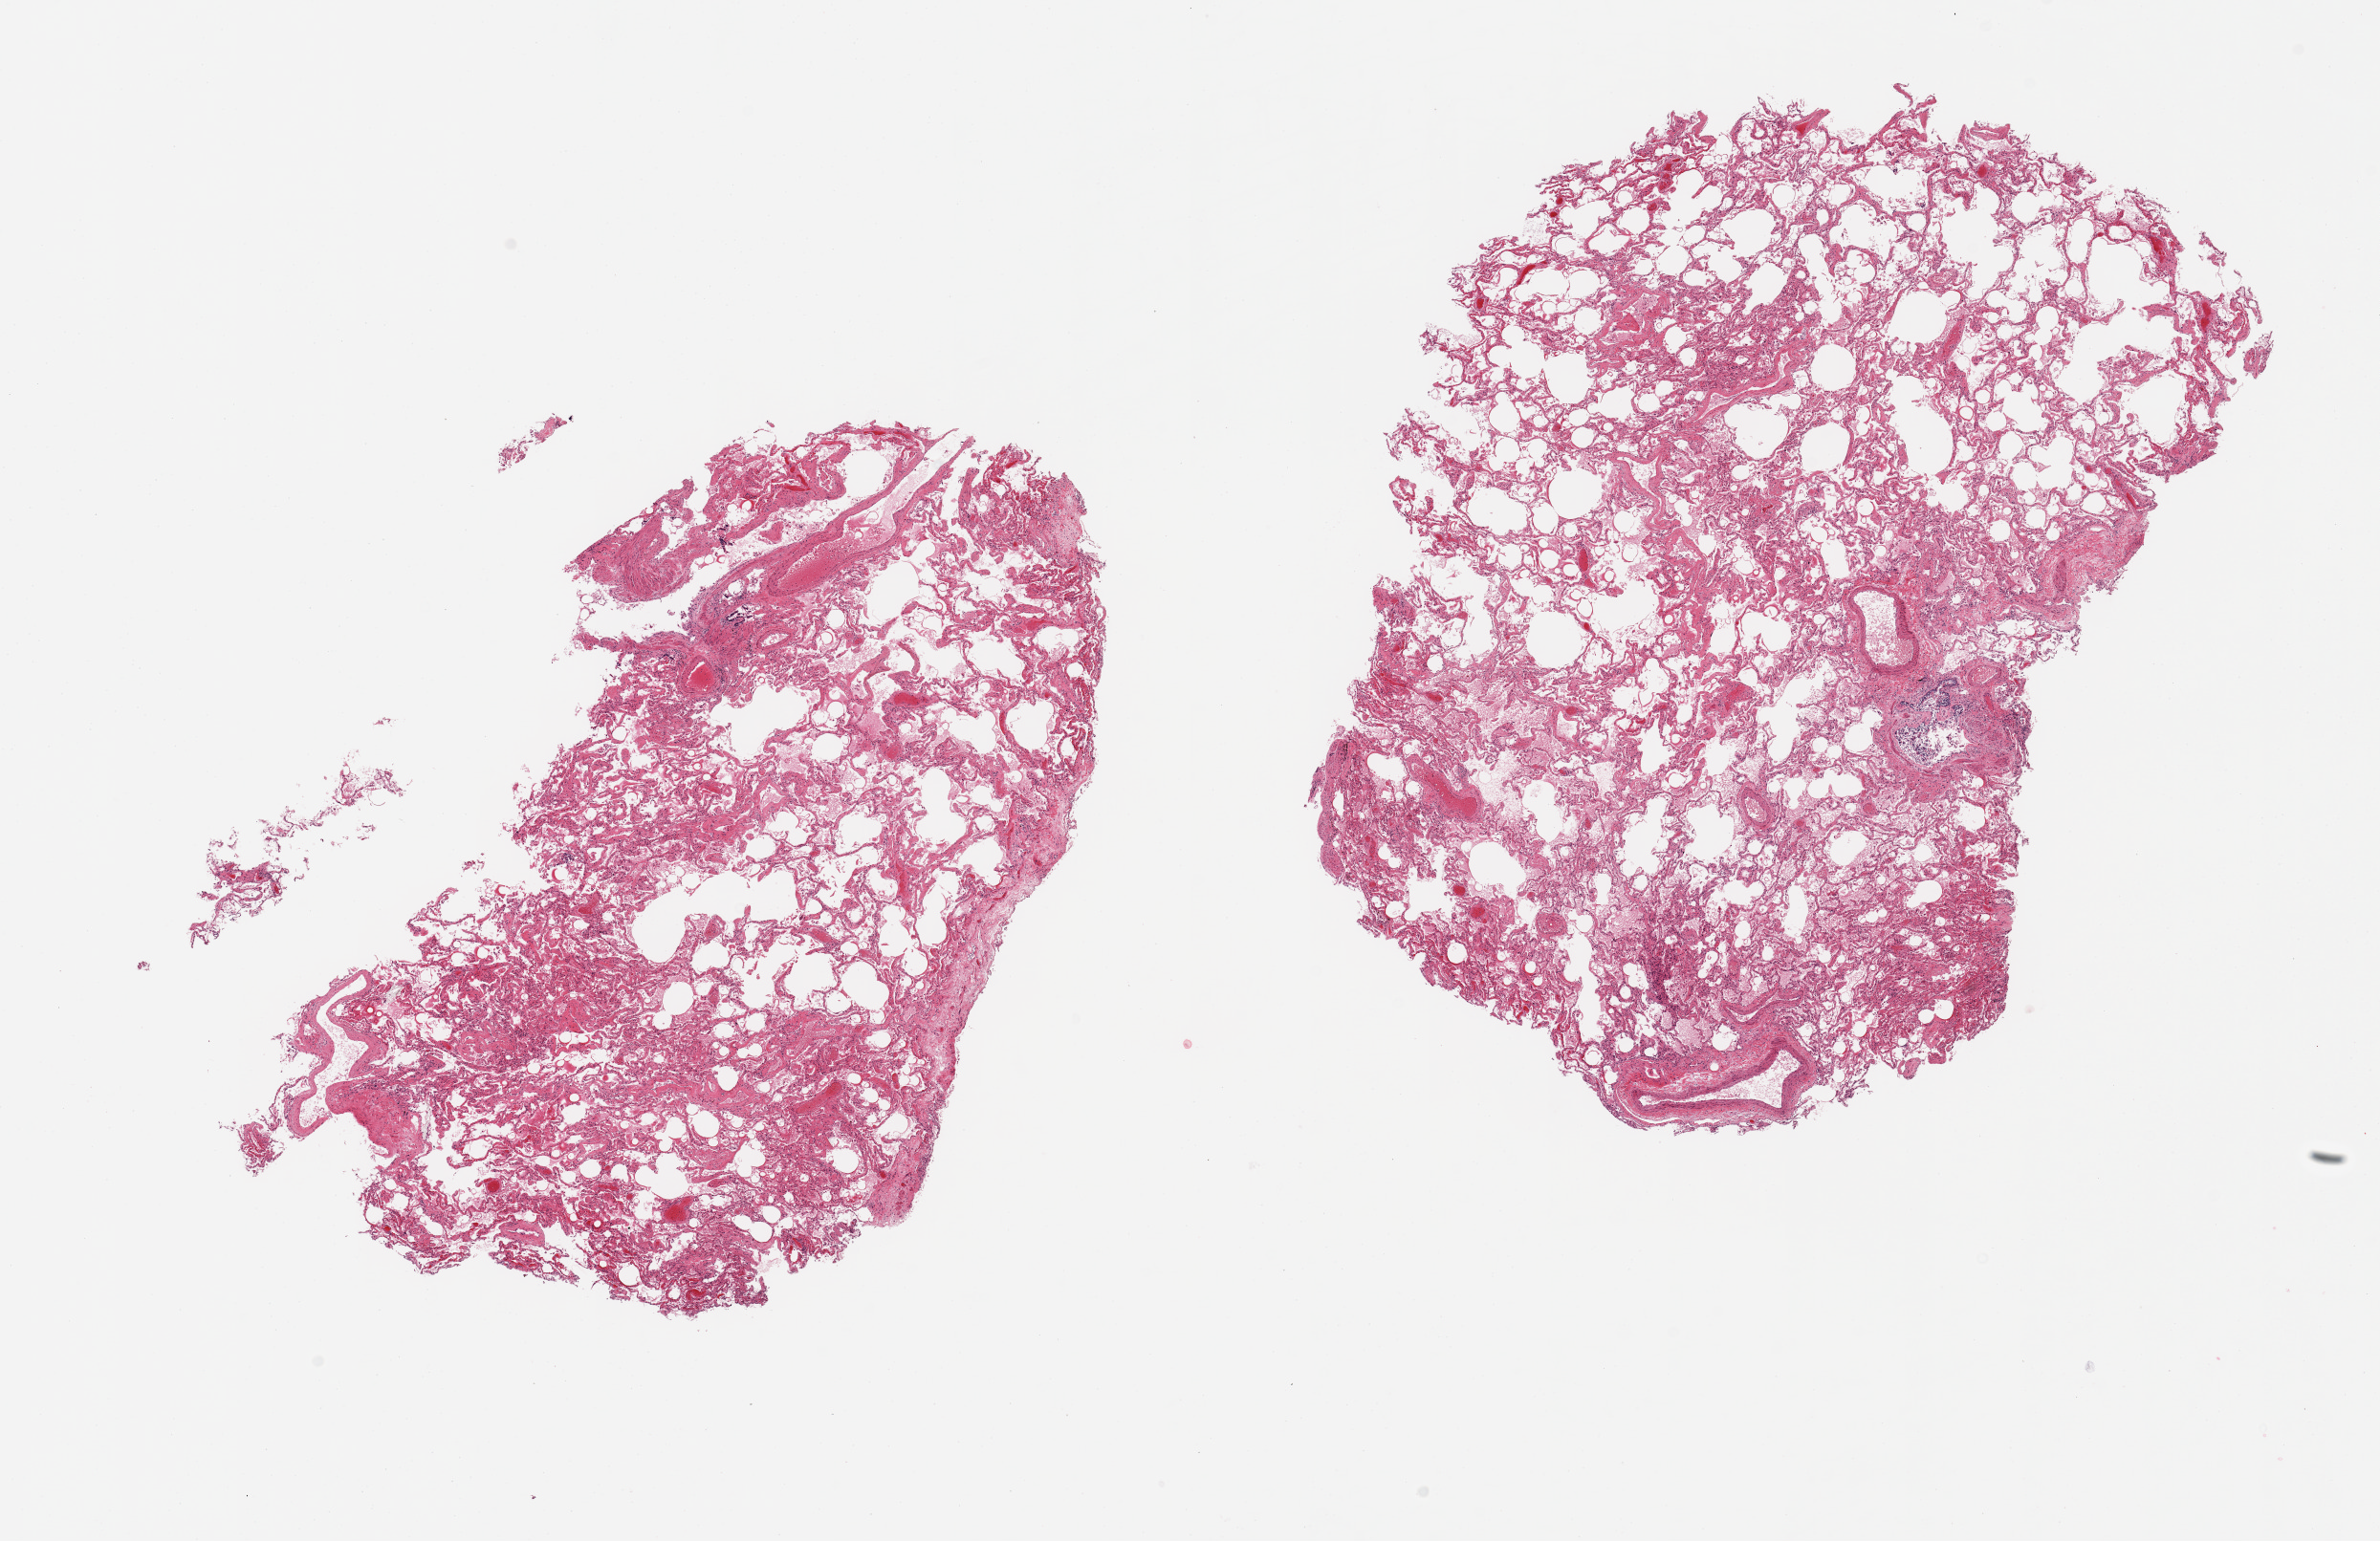
Digitized H&E-stained section, brightfield — a low-resolution overview of the entire scanned area, about 19.7 x 12.8 mm. PAXgene-fixed paraffin-embedded (PFPE) section. Section of lung (target tissue). Donor tissue sample.
Review note (as recorded): 2 pieces, mild congestion.